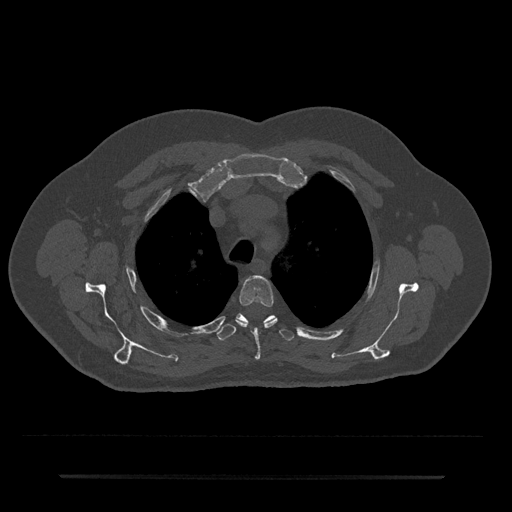
CT including the spine, one axial slice. Position 554 of 797 along the scan axis. Reconstruction kernel Br40s/3. 120 kVp. Bone window (W 1800 / L 400 HU). 0.5 mm slice thickness. 512 × 512 image matrix, field of view 437 × 437 mm. Patient: male, 69 years. Case-level facts recorded for this patient, not image findings: primary cancer: prostate.
Outlined on this slice (semi-automatically segmented with operator editing):
- T3 vertebra: box from (x=236, y=276) to (x=278, y=360) px
- T4 vertebra: (x=217, y=313)–(x=294, y=341)